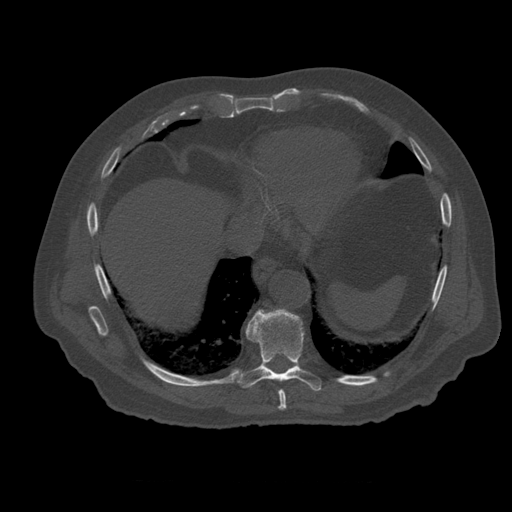
CT including the spine, one axial slice. Slice 323 of 399 in the series (ordered by position). Reconstruction kernel STANDARD. 120 kVp. Bone window (W 1800 / L 400 HU). 1.25 mm slice thickness. 512 × 512 image matrix, field of view 407 × 407 mm. Patient age 73 years. From the clinical record (not read from this slice): primary cancer: prostate.
Structures marked on this image (semi-automatically segmented with operator editing):
- T8 vertebra: bounding box (x1, y1, x2, y2) in pixels: (279, 390, 287, 413)
- T9 vertebra: (236, 309, 322, 391)